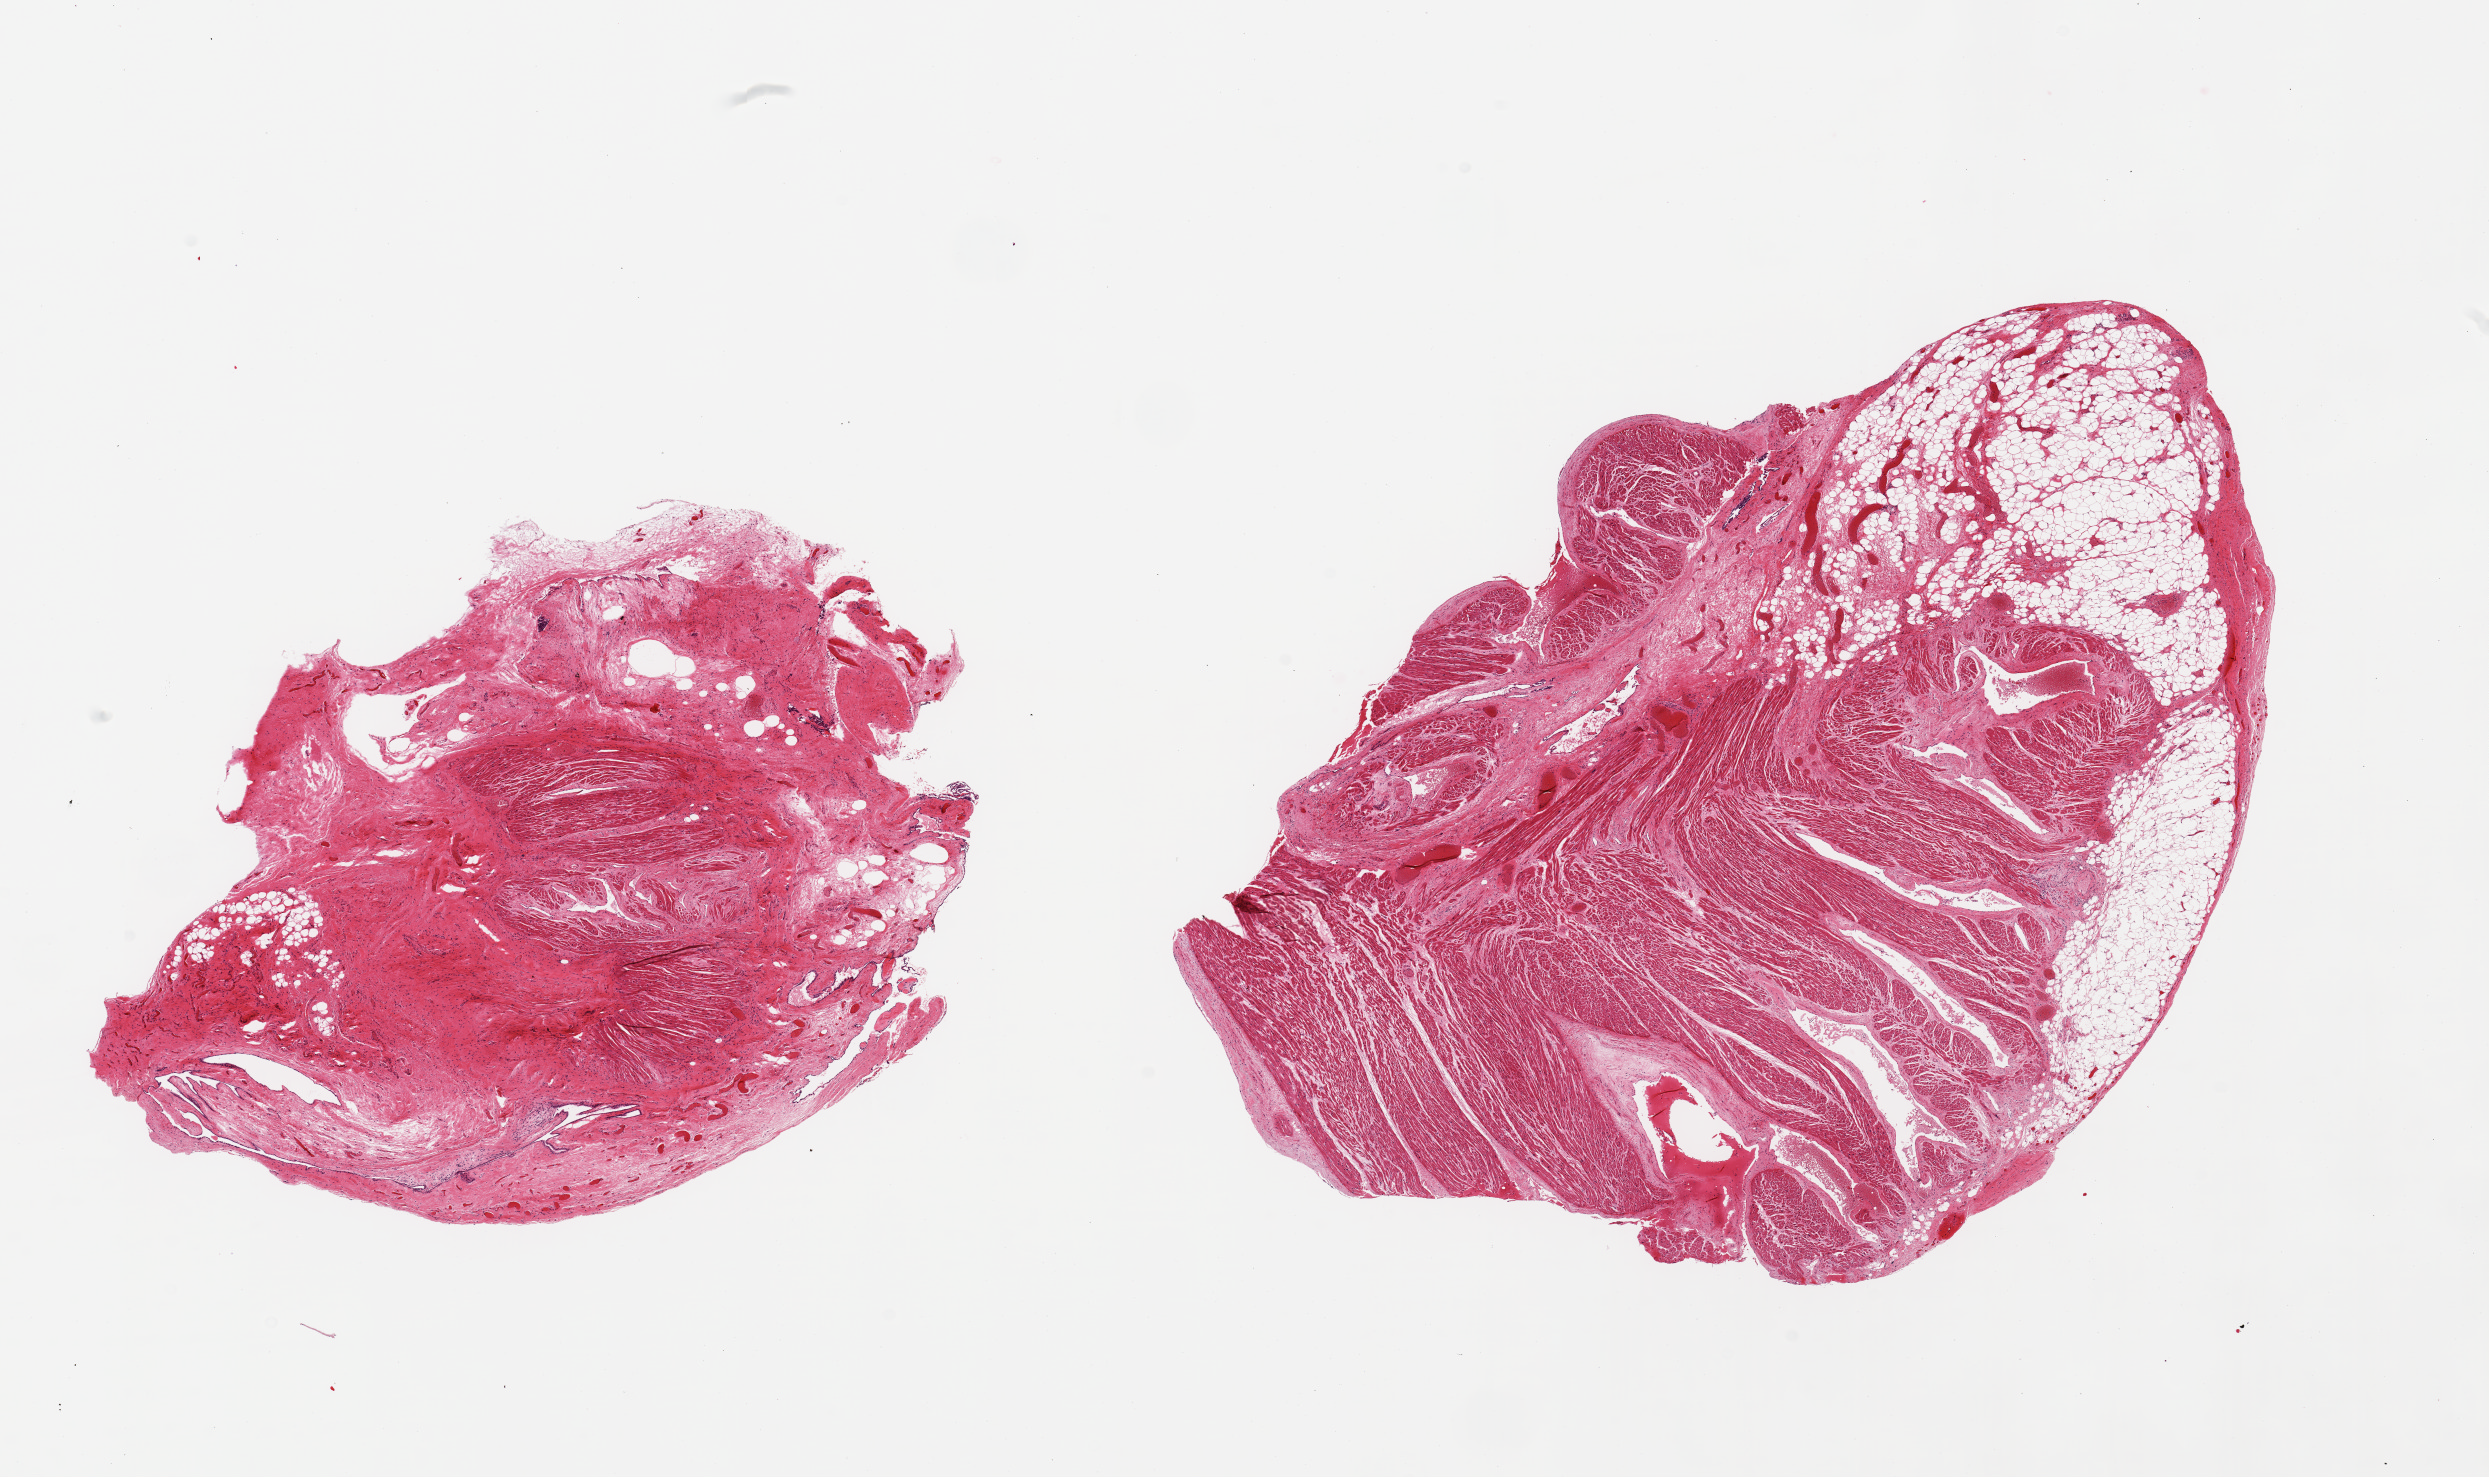
H&E whole-slide image — whole scanned area (about 19.7 x 11.7 mm, acquisition: 20x scan) shown as a low-resolution overview. PAXgene-fixed, paraffin-embedded tissue. Sampled site (target tissue): auricular appendage. Donor tissue sample. Donor: male.
* review note (as recorded): 2 pieces, no abnormalities